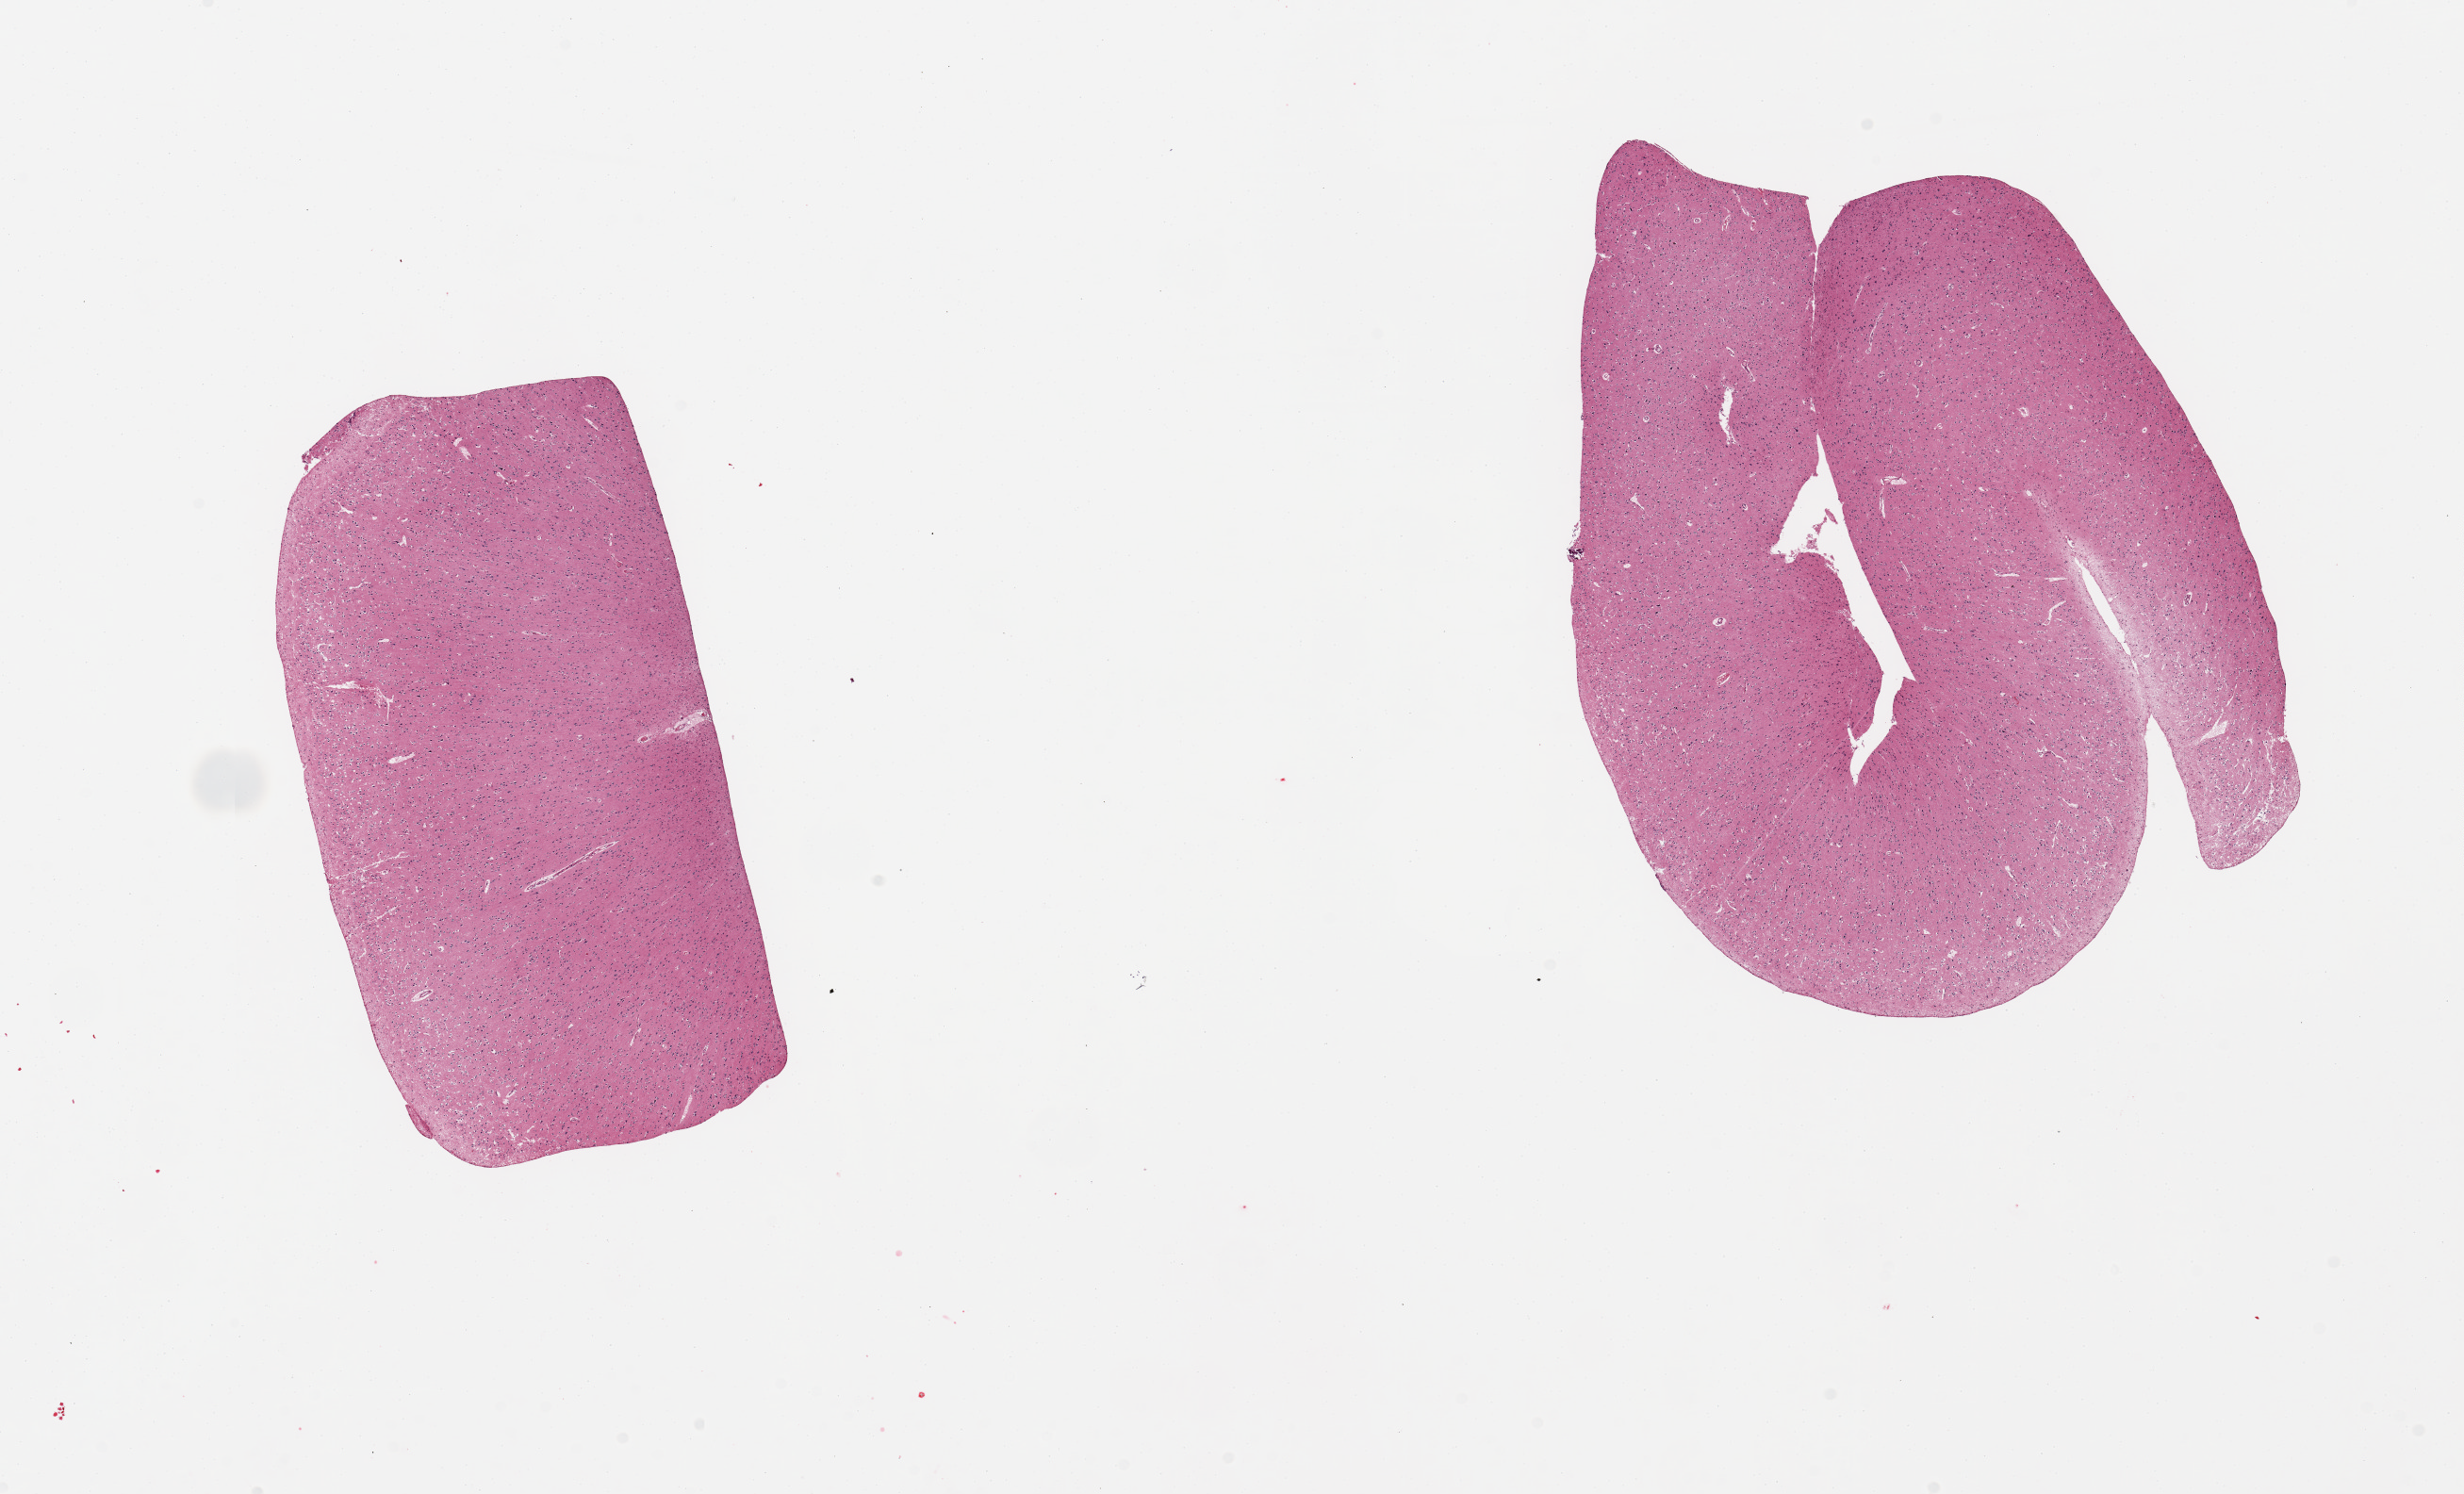
Whole-slide image, hematoxylin and eosin (H&E) stain — a low-resolution overview of the entire scanned area, about 20.7 x 12.5 mm (acquisition: 20x scan). PAXgene-fixed, paraffin-embedded tissue. Target tissue: cerebral cortex. Tissue donor sample. Donor: male.
Pathologist's review note for this sample: 2 pieces, no abnormalities.